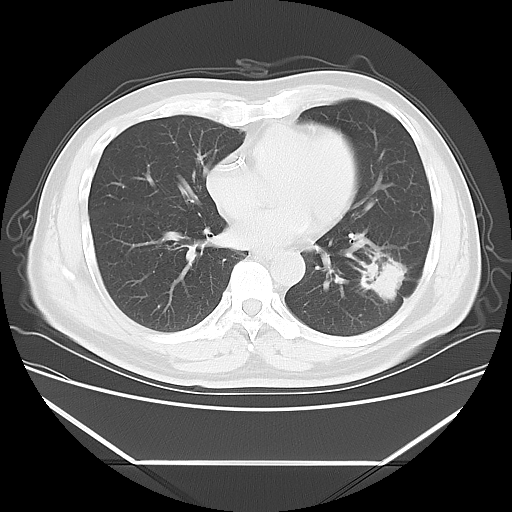
Chest CT, one axial slice; position 25 of 57 along the scan axis; reconstruction kernel LUNG; 120 kVp; lung window (W 1500 / L -600 HU); 512 × 512 image matrix, field of view 384 × 384 mm. Patient: male, 53 years. From the clinical record (not read from this slice): clinical TNM (as recorded): T1c N0 M0; histopathological grade: G2-3.
Structures marked on this image (bounding box drawn by a radiologist):
- lung tumour (recorded histology: adenocarcinoma): box from (x=360, y=239) to (x=409, y=304) px